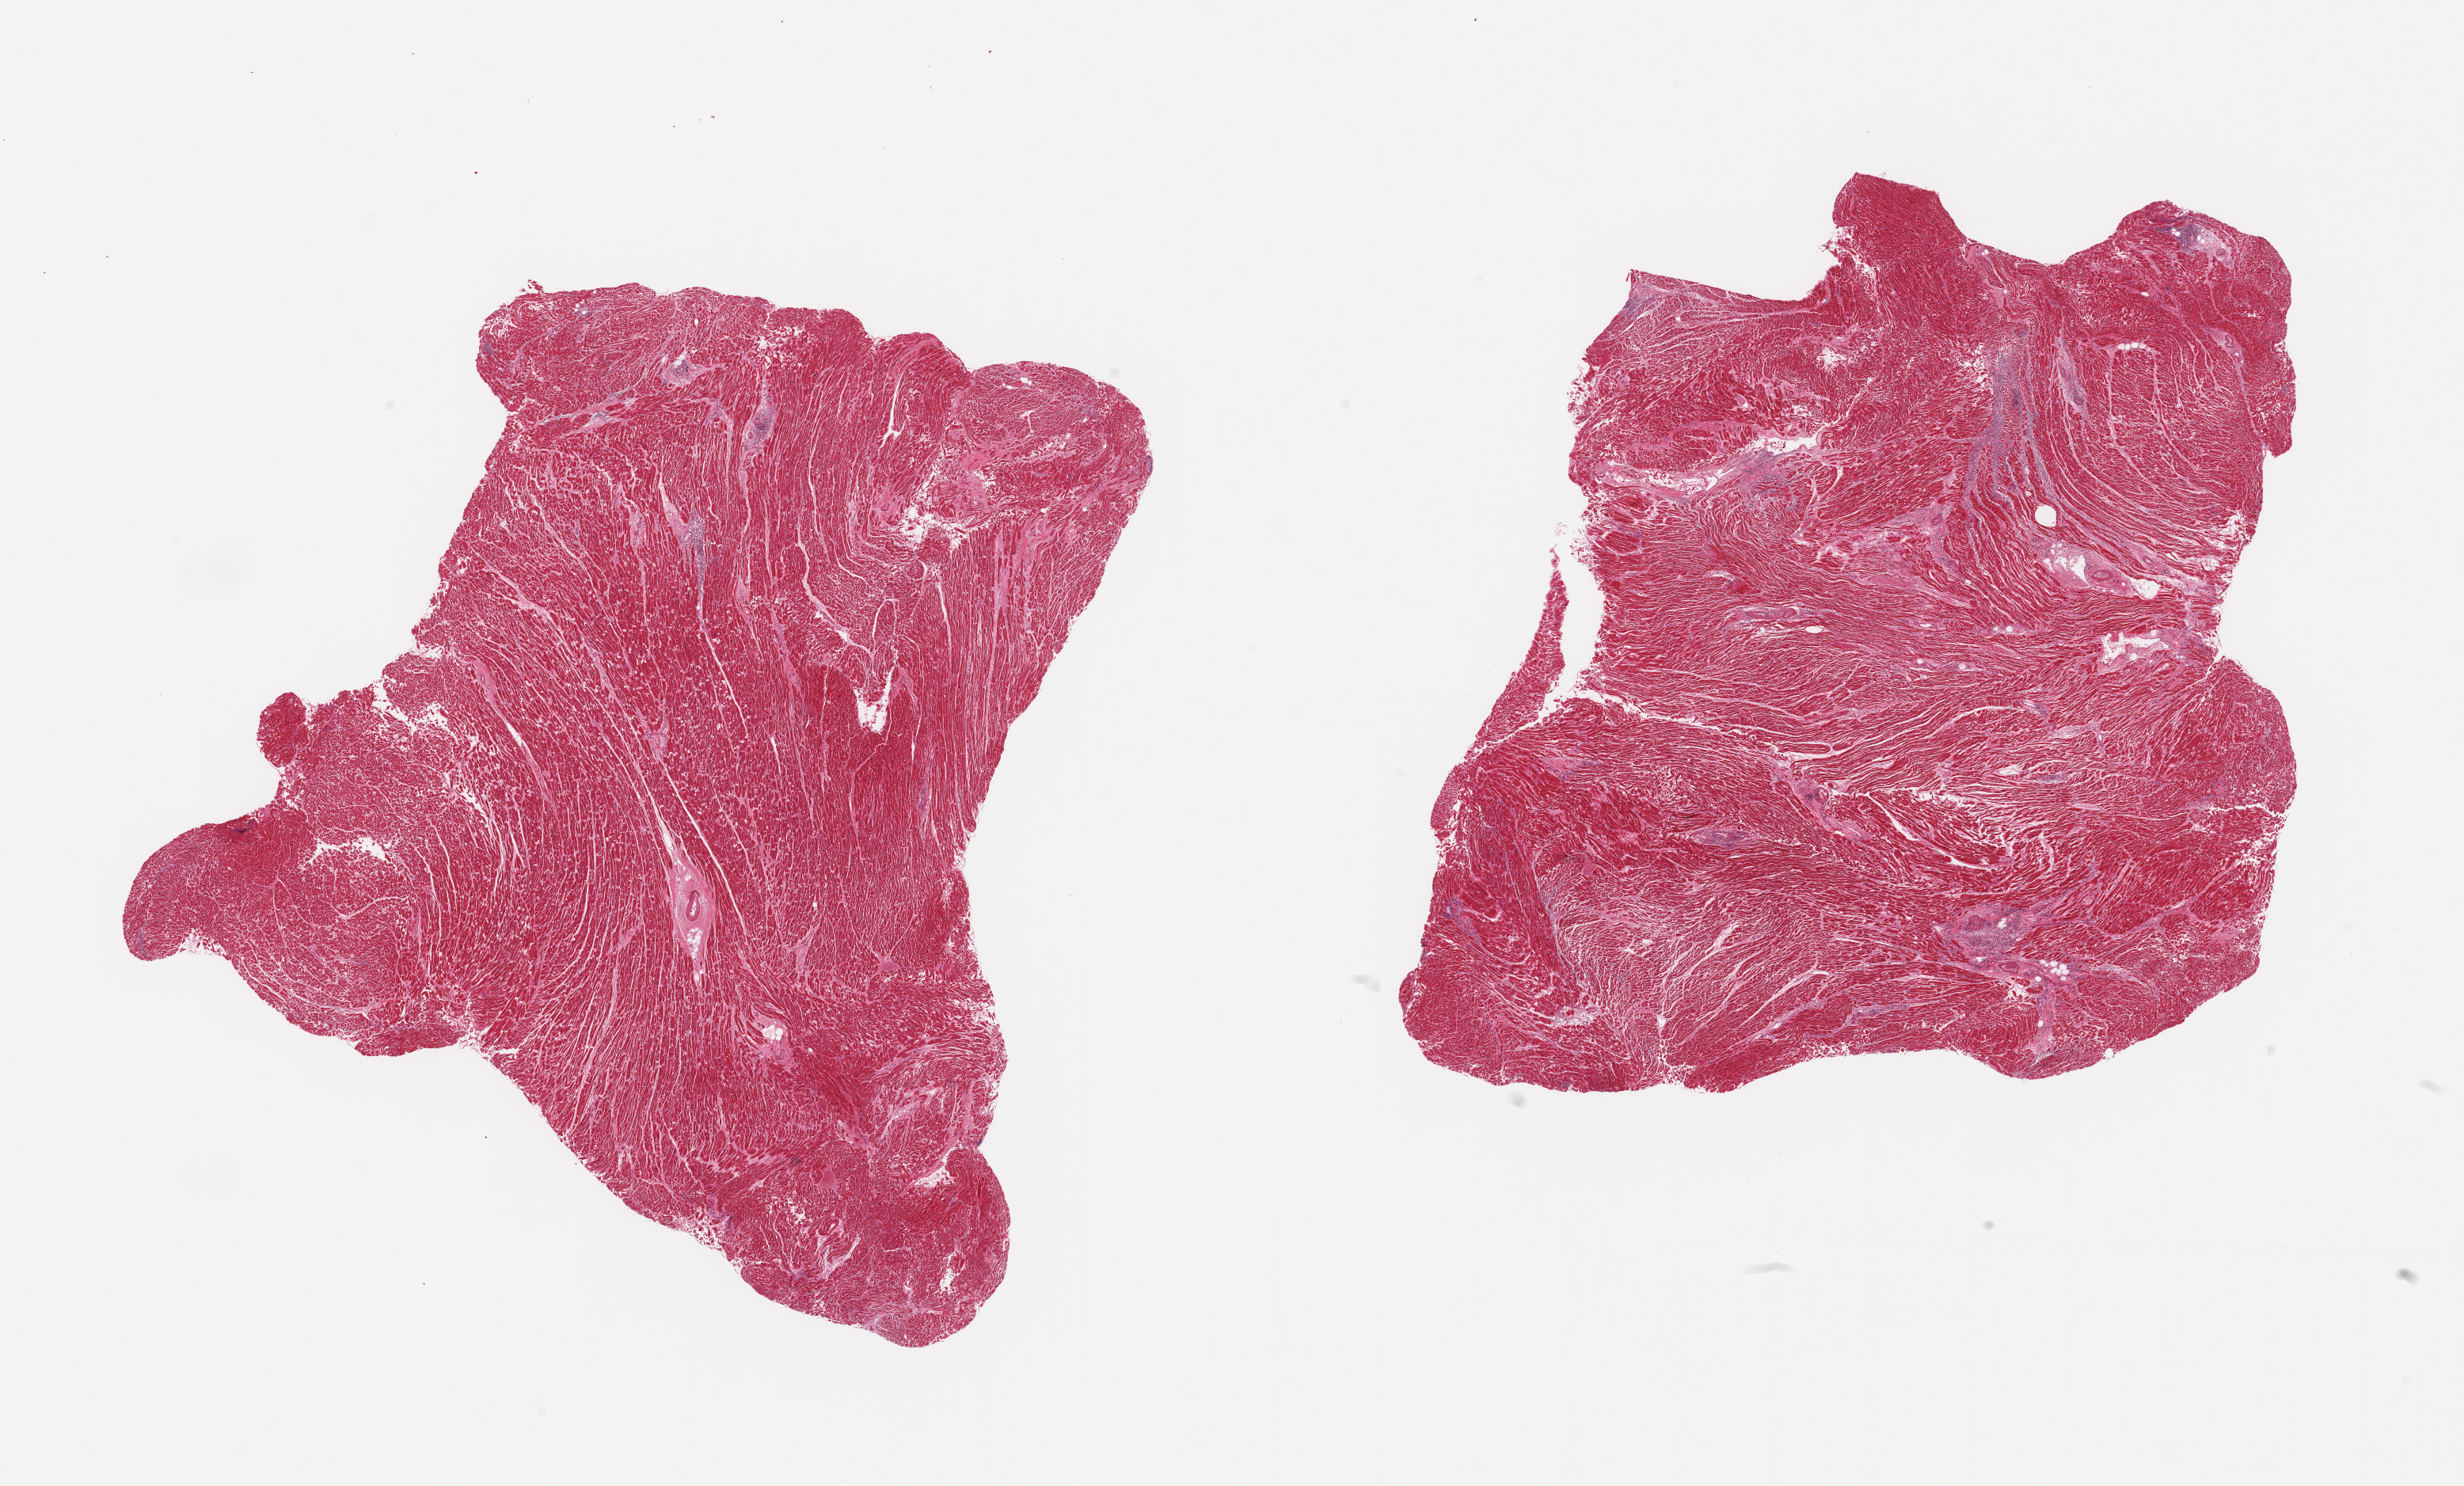
Digitized H&E-stained section — whole scanned area (about 24.6 x 14.8 mm) shown as a low-resolution overview, PAXgene-fixed, paraffin-embedded tissue, sampled site (target tissue): heart, tissue donor sample. Donor: male.
• pathologist's review note for this sample: 2 pieces, subacute infarcts with leukocytic infiltrates and hyperemia